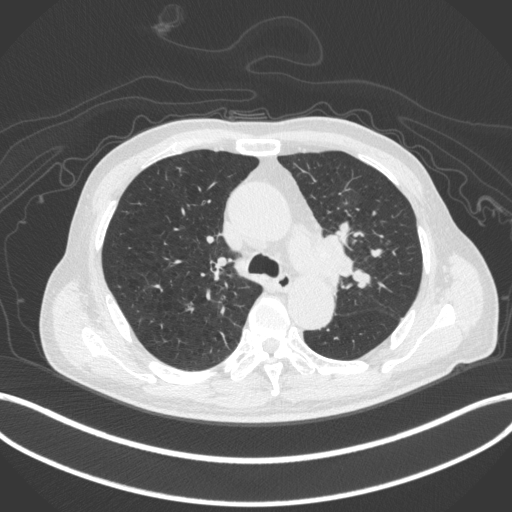
Chest CT, one axial slice. Slice 295 of 420 in the series (ordered by position). Reconstruction kernel B31f. Lung window (W 1500 / L -600 HU). 1 mm slice thickness. 512 × 512 image matrix, field of view 400 × 400 mm. Patient: male, 77 years. Case-level facts recorded for this patient, not image findings: clinical TNM (as recorded): T3 N1 M0.
Structures marked on this image (bounding box drawn by a radiologist):
- lung tumour (recorded histology: adenocarcinoma): bounding box (x1, y1, x2, y2) in pixels: (304, 234, 353, 281)